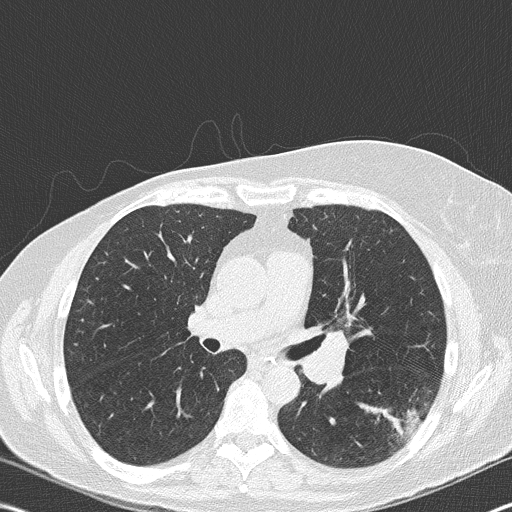
Low-dose screening chest CT, one axial slice; slice 105 of 177 in the series (ordered by position); reconstruction kernel B50f; 120 kVp; lung window (W 1500 / L -600 HU); 2 mm slice thickness; 512 × 512 image matrix.
Annotated regions visible in this slice (expert manual segmentation):
- lesion 1 (tumor): bounding box (x1, y1, x2, y2) in pixels: (363, 405, 421, 440)
- lesion 2 (nodule, hilum of left lung): (304, 330, 346, 387)